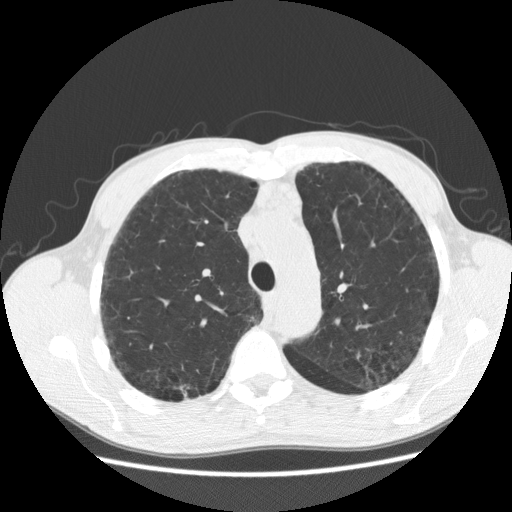
Low-dose screening chest CT, one axial slice; slice 141 of 195 in the series (ordered by position); reconstruction kernel STANDARD; lung window (W 1500 / L -600 HU); 512 × 512 image matrix, field of view 355 × 355 mm.
Outlined on this slice (outlined manually by an expert reader):
- lesion 1 (tumor, upper lobe of right lung): bounding box [x1, y1, x2, y2] px = [181, 385, 190, 396]